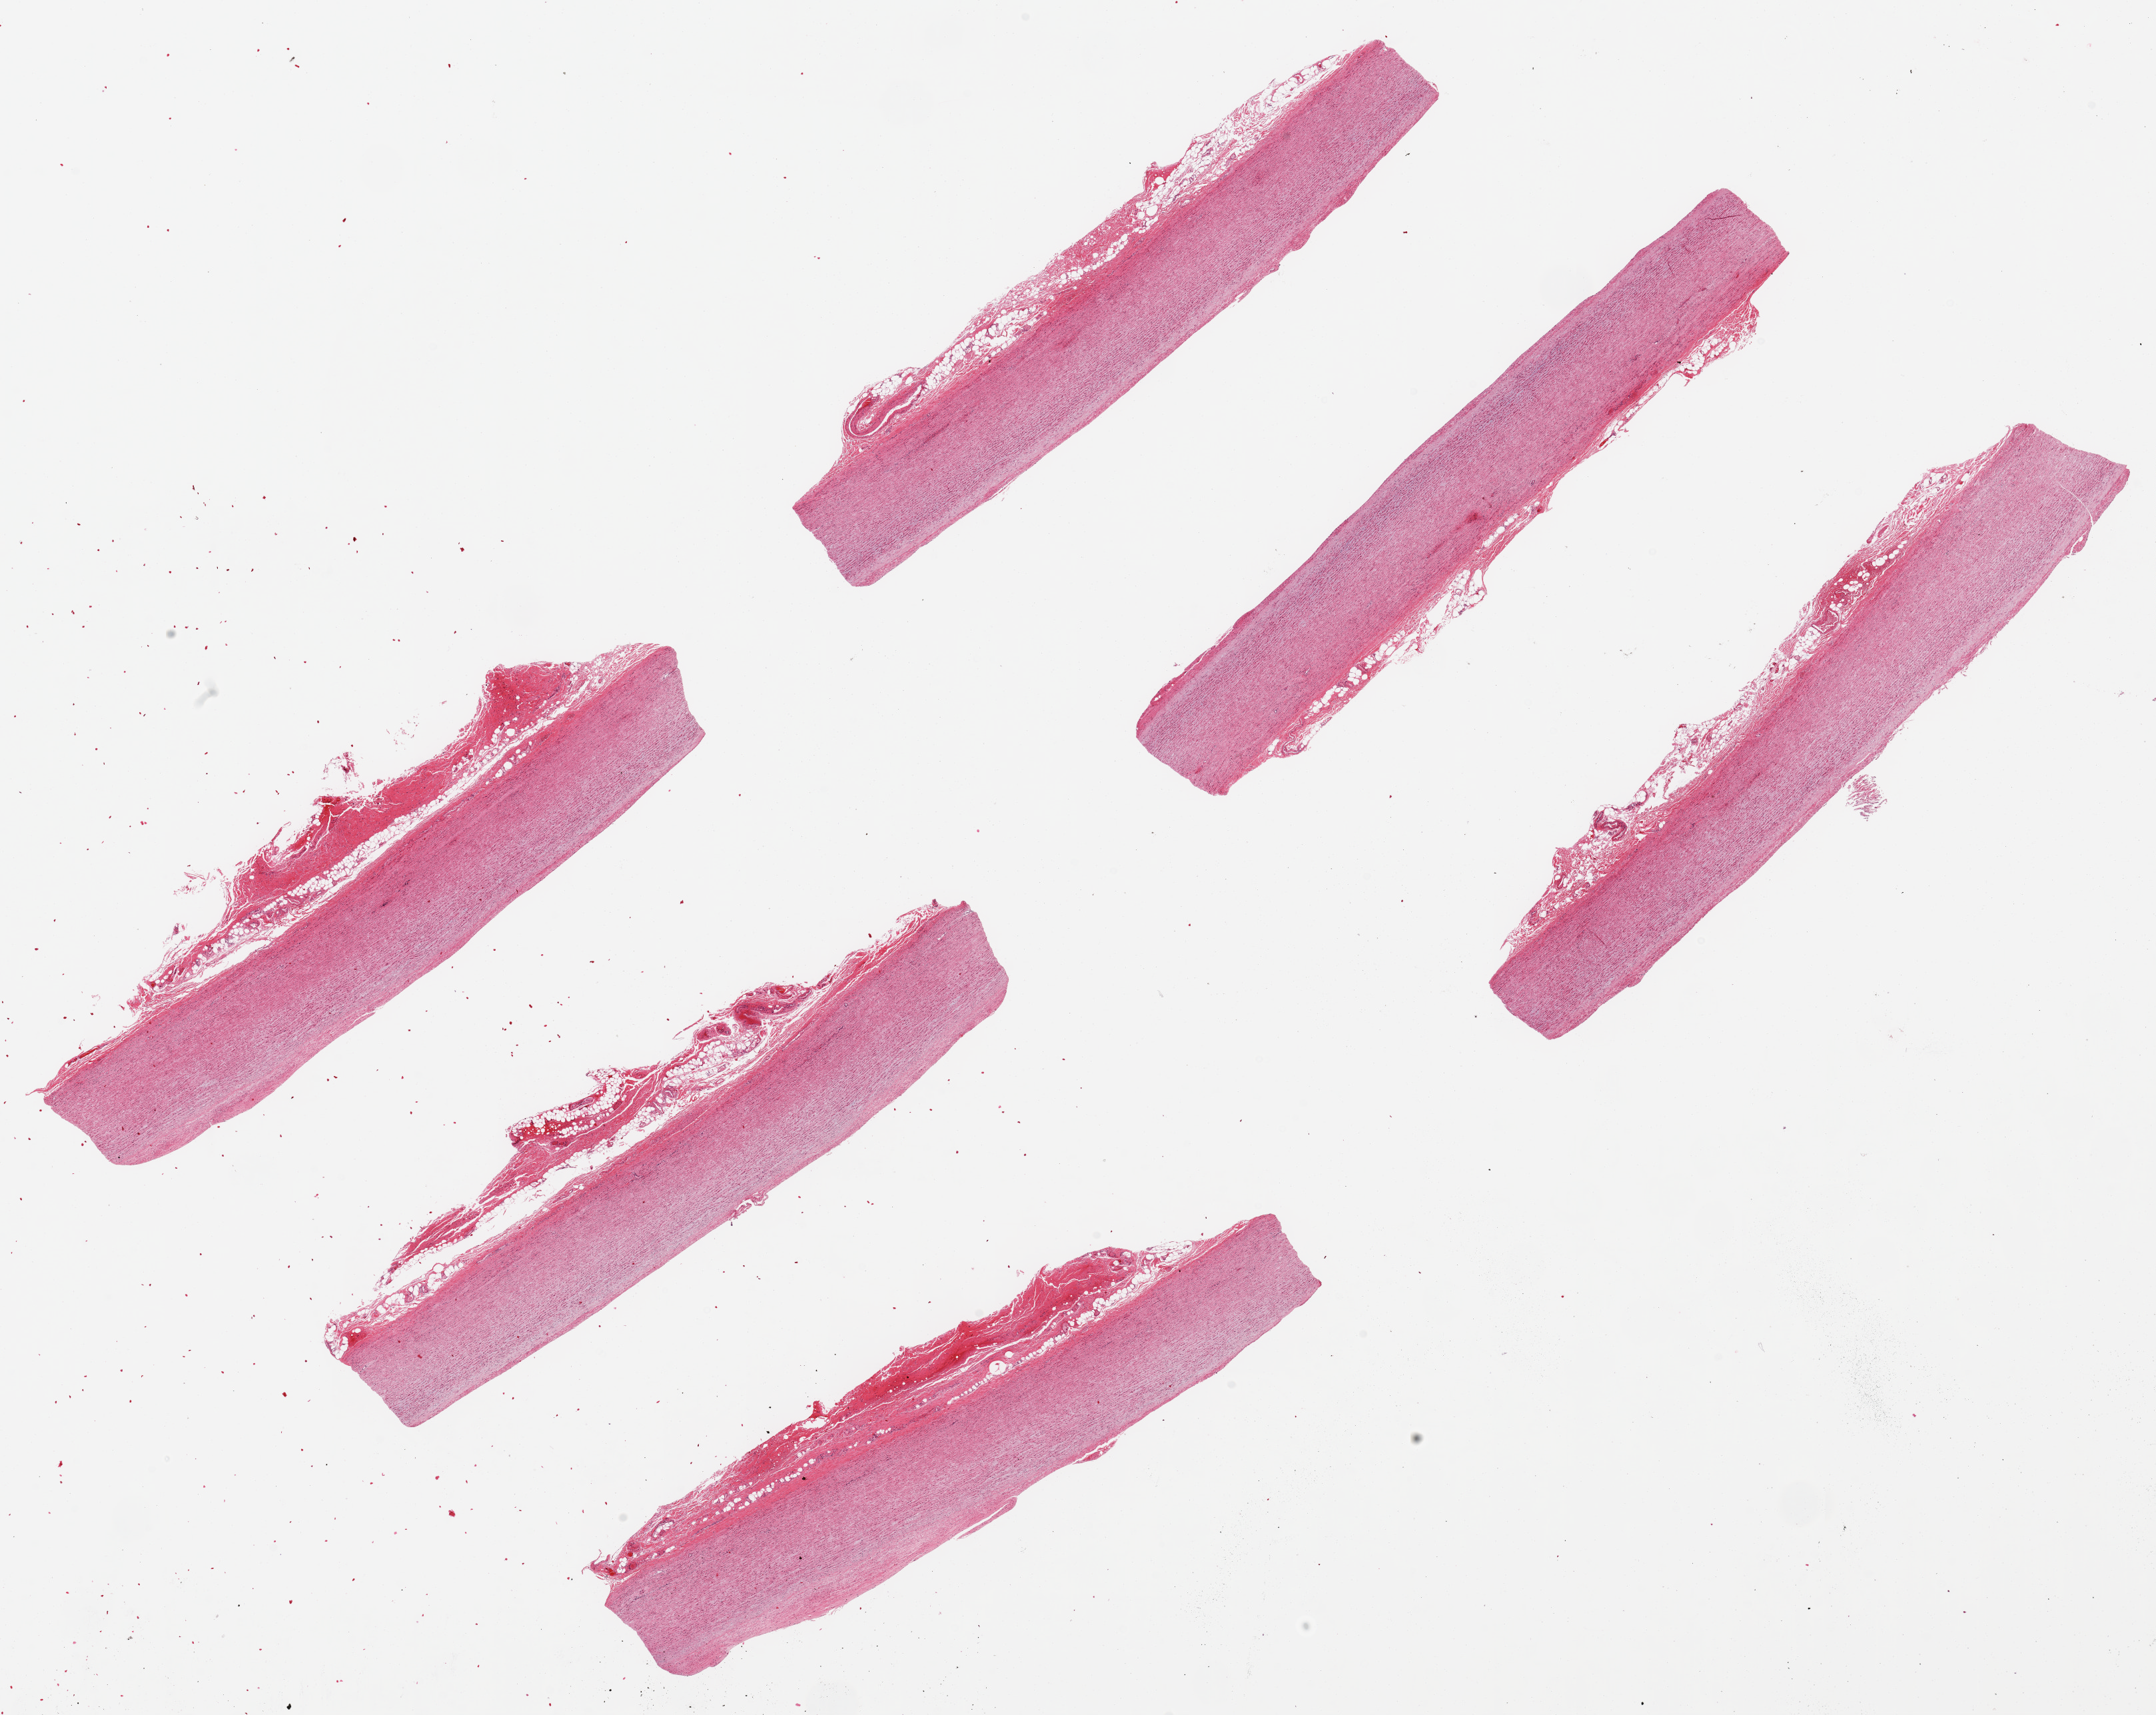
Digitized H&E-stained section, a low-resolution overview of the entire scanned area, about 25.6 x 20.4 mm (from a 20x scan); PAXgene-fixed paraffin-embedded (PFPE) section; sampled site (target tissue): aorta; tissue donor sample. Donor: female.
Reviewer comment on this tissue sample: 6 ~9x1.5mm pieces, minimal atherosis.